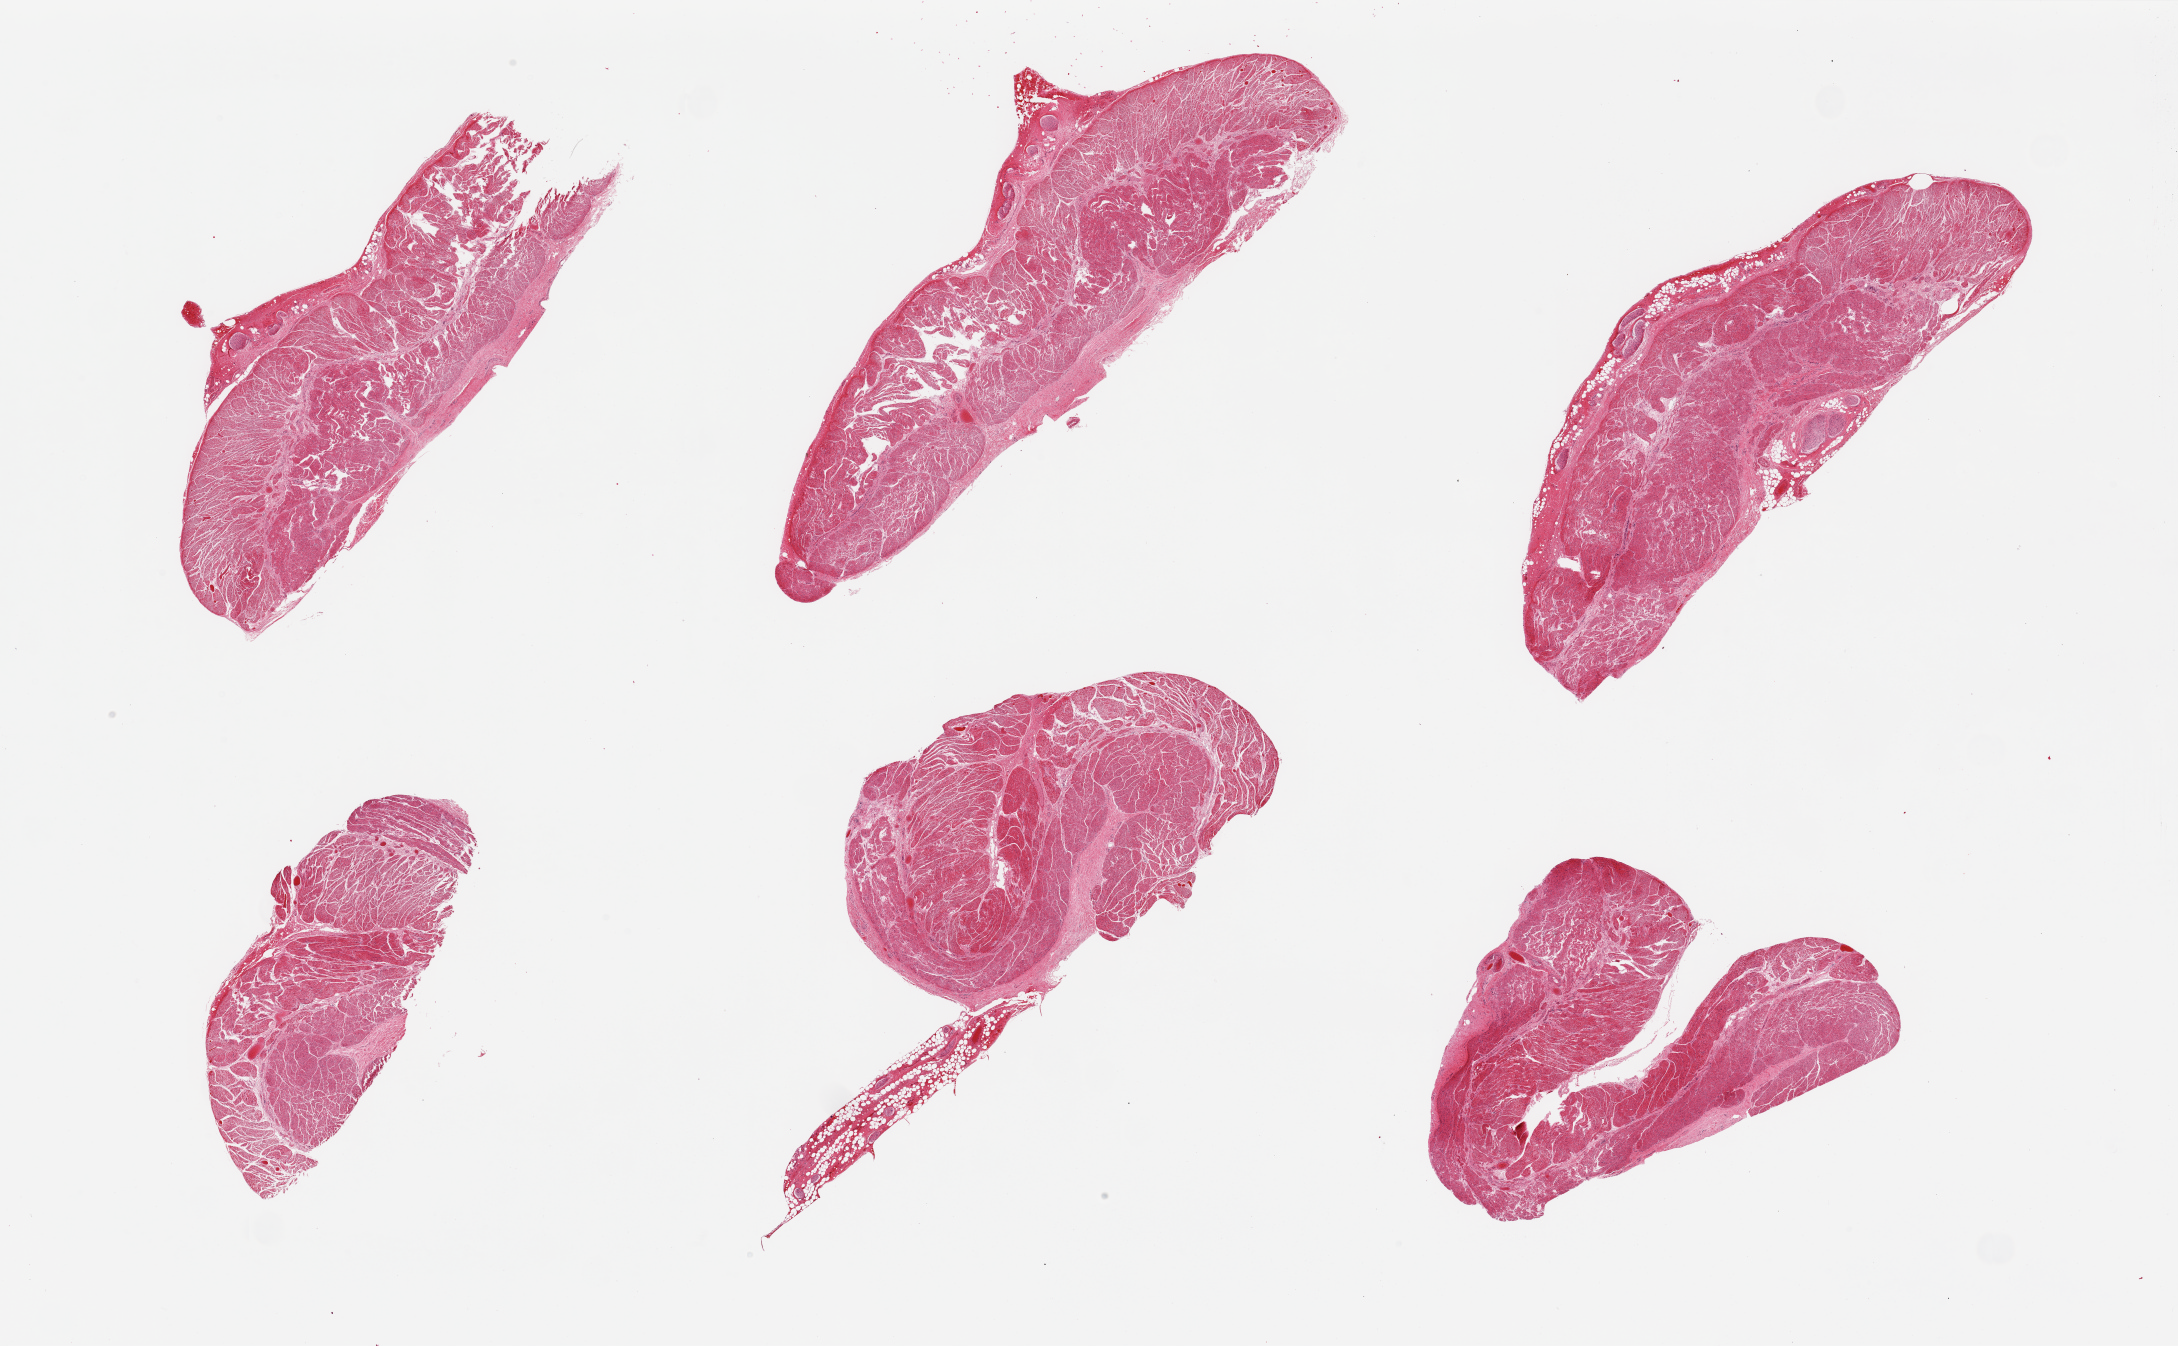
Digitized hematoxylin and eosin (H&E)-stained section — whole scanned area (about 34.5 x 21.3 mm) shown as a low-resolution overview; PAXgene-fixed, paraffin-embedded tissue; section of esophageal muscle (target tissue); donor tissue sample. Donor sex: female.
Pathologist's review note for this sample: 6 pieces.